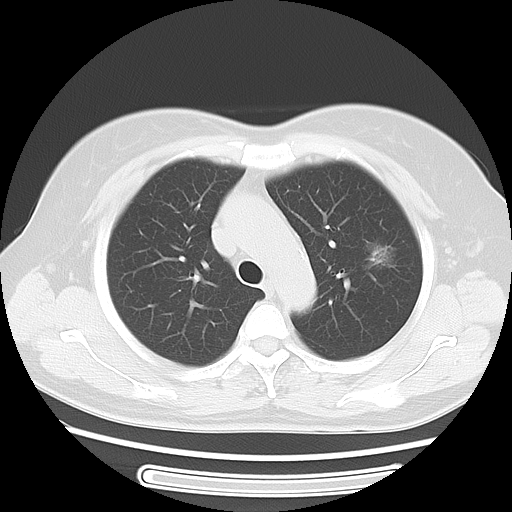
Chest CT, one axial slice; slice 36 of 52 in the series (ordered by position); reconstruction kernel LUNG; 120 kVp; lung window (W 1500 / L -600 HU); 5 mm slice thickness; 512 × 512 image matrix, field of view 350 × 350 mm. Female patient, age 54 years. From the clinical record (not read from this slice): clinical TNM (as recorded): T1c N0 M0; histopathological grade: G1.
Annotated regions visible in this slice (rectangle marked by the reading radiologist):
- lung tumour (recorded histology: adenocarcinoma): bounding box [x1, y1, x2, y2] px = [357, 233, 405, 286]